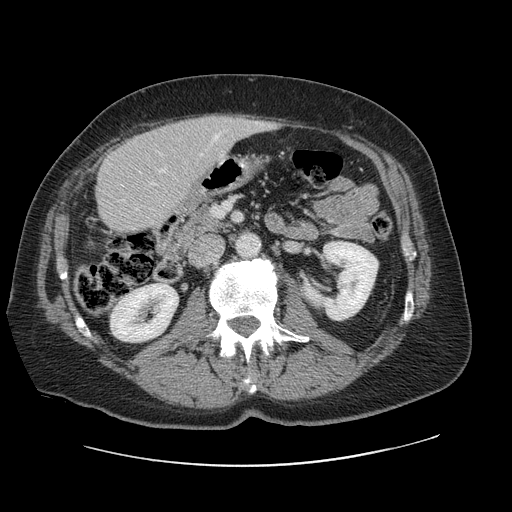
Contrast-enhanced abdominal CT, one axial slice; position 32 of 138 along the scan axis; 120 kVp; intravenous contrast given; soft-tissue window (W 400 / L 40 HU); 512 × 512 image matrix, field of view 402 × 402 mm. Male patient, age 71 years. Case-level facts recorded for this patient, not image findings: diagnosis: colorectal cancer liver metastases, imaged before liver resection; multiple liver metastases: no; largest metastasis: 3.3 cm; disease in both lobes: no.
Structures marked on this image (outlined manually by an expert reader):
- hepatic veins: box from (x=201, y=135) to (x=219, y=156) px
- liver: (x=97, y=116)–(x=268, y=235)
- planned liver remnant (the part of the liver to remain after resection): (x=97, y=133)–(x=186, y=234)
- portal vein (with intrahepatic branches): (x=159, y=169)–(x=165, y=172)